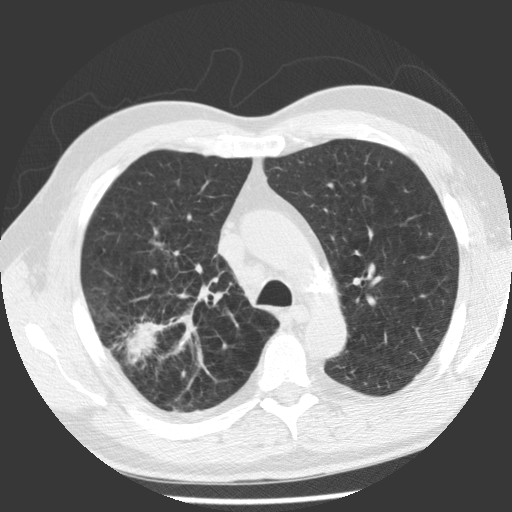
Low-dose screening chest CT, axial slice, baseline annual screen, lung window (W 1500 / L -600 HU), 512 × 512 image matrix, field of view 344 × 344 mm. Male, age 62 years at enrolment.
Expert reader's lesion annotation, bounding box [x1, y1, x2, y2] px = [109, 300, 184, 372]. The screening reader recorded 2 non-calcified nodules or masses ≥4 mm on this exam (right upper lobe, right upper lobe); which of them this box marks is not recorded. Participant outcome: lung cancer diagnosed 71 days after this screen — adenocarcinoma, NOS, right upper lobe, poorly differentiated (G3), stage IV (AJCC 6th edition), 30 mm at pathology.